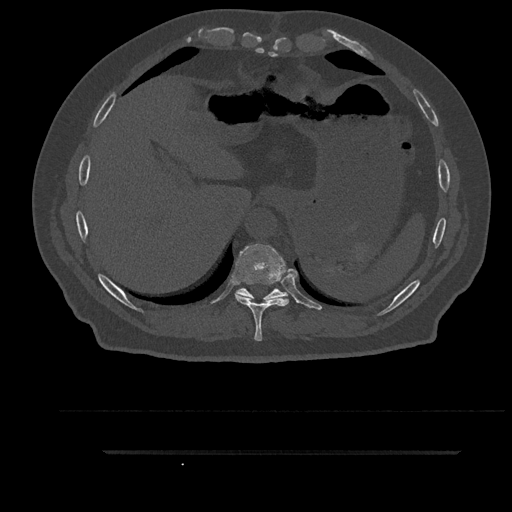
CT including the spine, one axial slice. Slice 401 of 797 in the series (ordered by position). Bone window (W 1800 / L 400 HU). 512 × 512 image matrix. Patient: male, 63 years. Case-level facts recorded for this patient, not image findings: primary cancer: renal; vertebrae with lytic lesions (as recorded): T8.
Outlined on this slice (semi-automatically segmented with operator editing):
- T10 vertebra: bounding box <235,288,288,301> (left, top, right, bottom; pixels)
- T9 vertebra: <234,243,289,341>